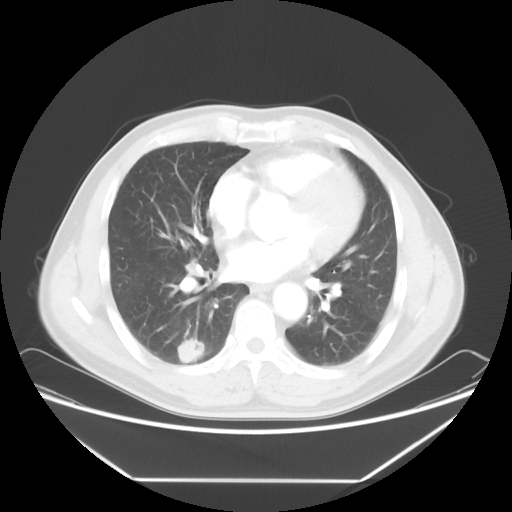
Chest CT, one axial slice; position 31 of 65 along the scan axis; 120 kVp; lung window (W 1500 / L -600 HU); 5 mm slice thickness; 512 × 512 image matrix, field of view 418 × 418 mm. Male patient, age 50 years. Case-level facts recorded for this patient, not image findings: clinical TNM (as recorded): T1c N0 M0.
Structures marked on this image (rectangle marked by the reading radiologist):
- lung tumour (recorded histology: adenocarcinoma): box from (x=173, y=335) to (x=208, y=366) px